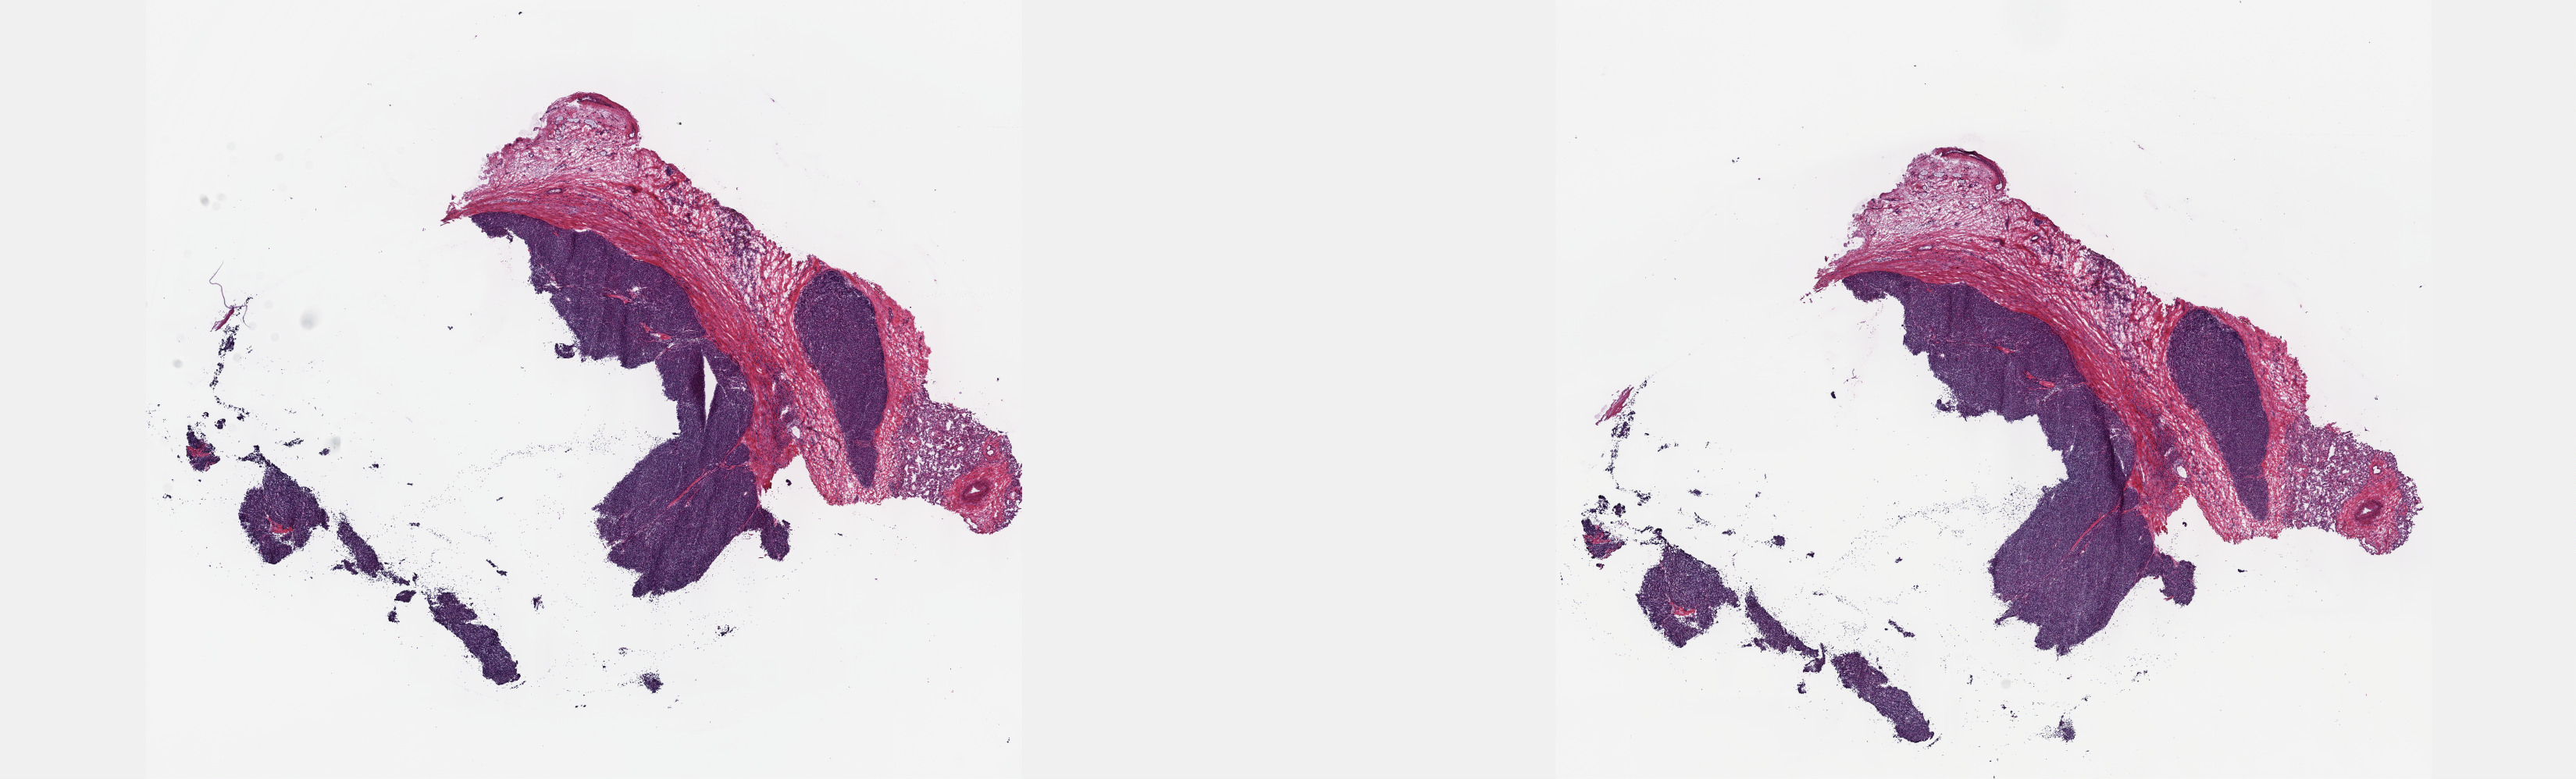
Whole-slide histology image, H&E, low-resolution overview of the scanned area, about 26.7 x 8.1 mm, frozen section from the top of the tissue portion, sample: primary tumour, thymus. Female patient; age at initial diagnosis 73 years. Composition of this section per pathologist review: tumour cells 50%, tumour nuclei 70%, normal cells 0%, stromal cells 50%, necrosis 0%. Infiltration values recorded for this section: lymphocyte infiltration 0%, monocyte infiltration 0%, neutrophil infiltration 0%.
- histologic diagnosis: Thymoma, type A, NOS (thorax, NOS)